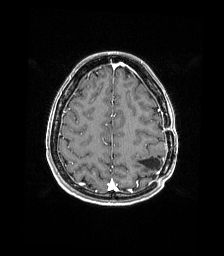
Brain MRI from a brain-tumour surgery series, one axial slice. Slice 51 of 176 in the series (ordered by position). T1-weighted post-contrast. 1 mm slice thickness. 224 × 256 image matrix, field of view 224 × 256 mm. From the clinical record (not read from this slice): histopathology: Atypical meningioma; WHO grade: 2; tumour location: Paramedian Left Parietal.
Structures marked on this image (manually delineated by an expert):
- previous resection cavity: bounding box <139,157,160,169> (left, top, right, bottom; pixels)